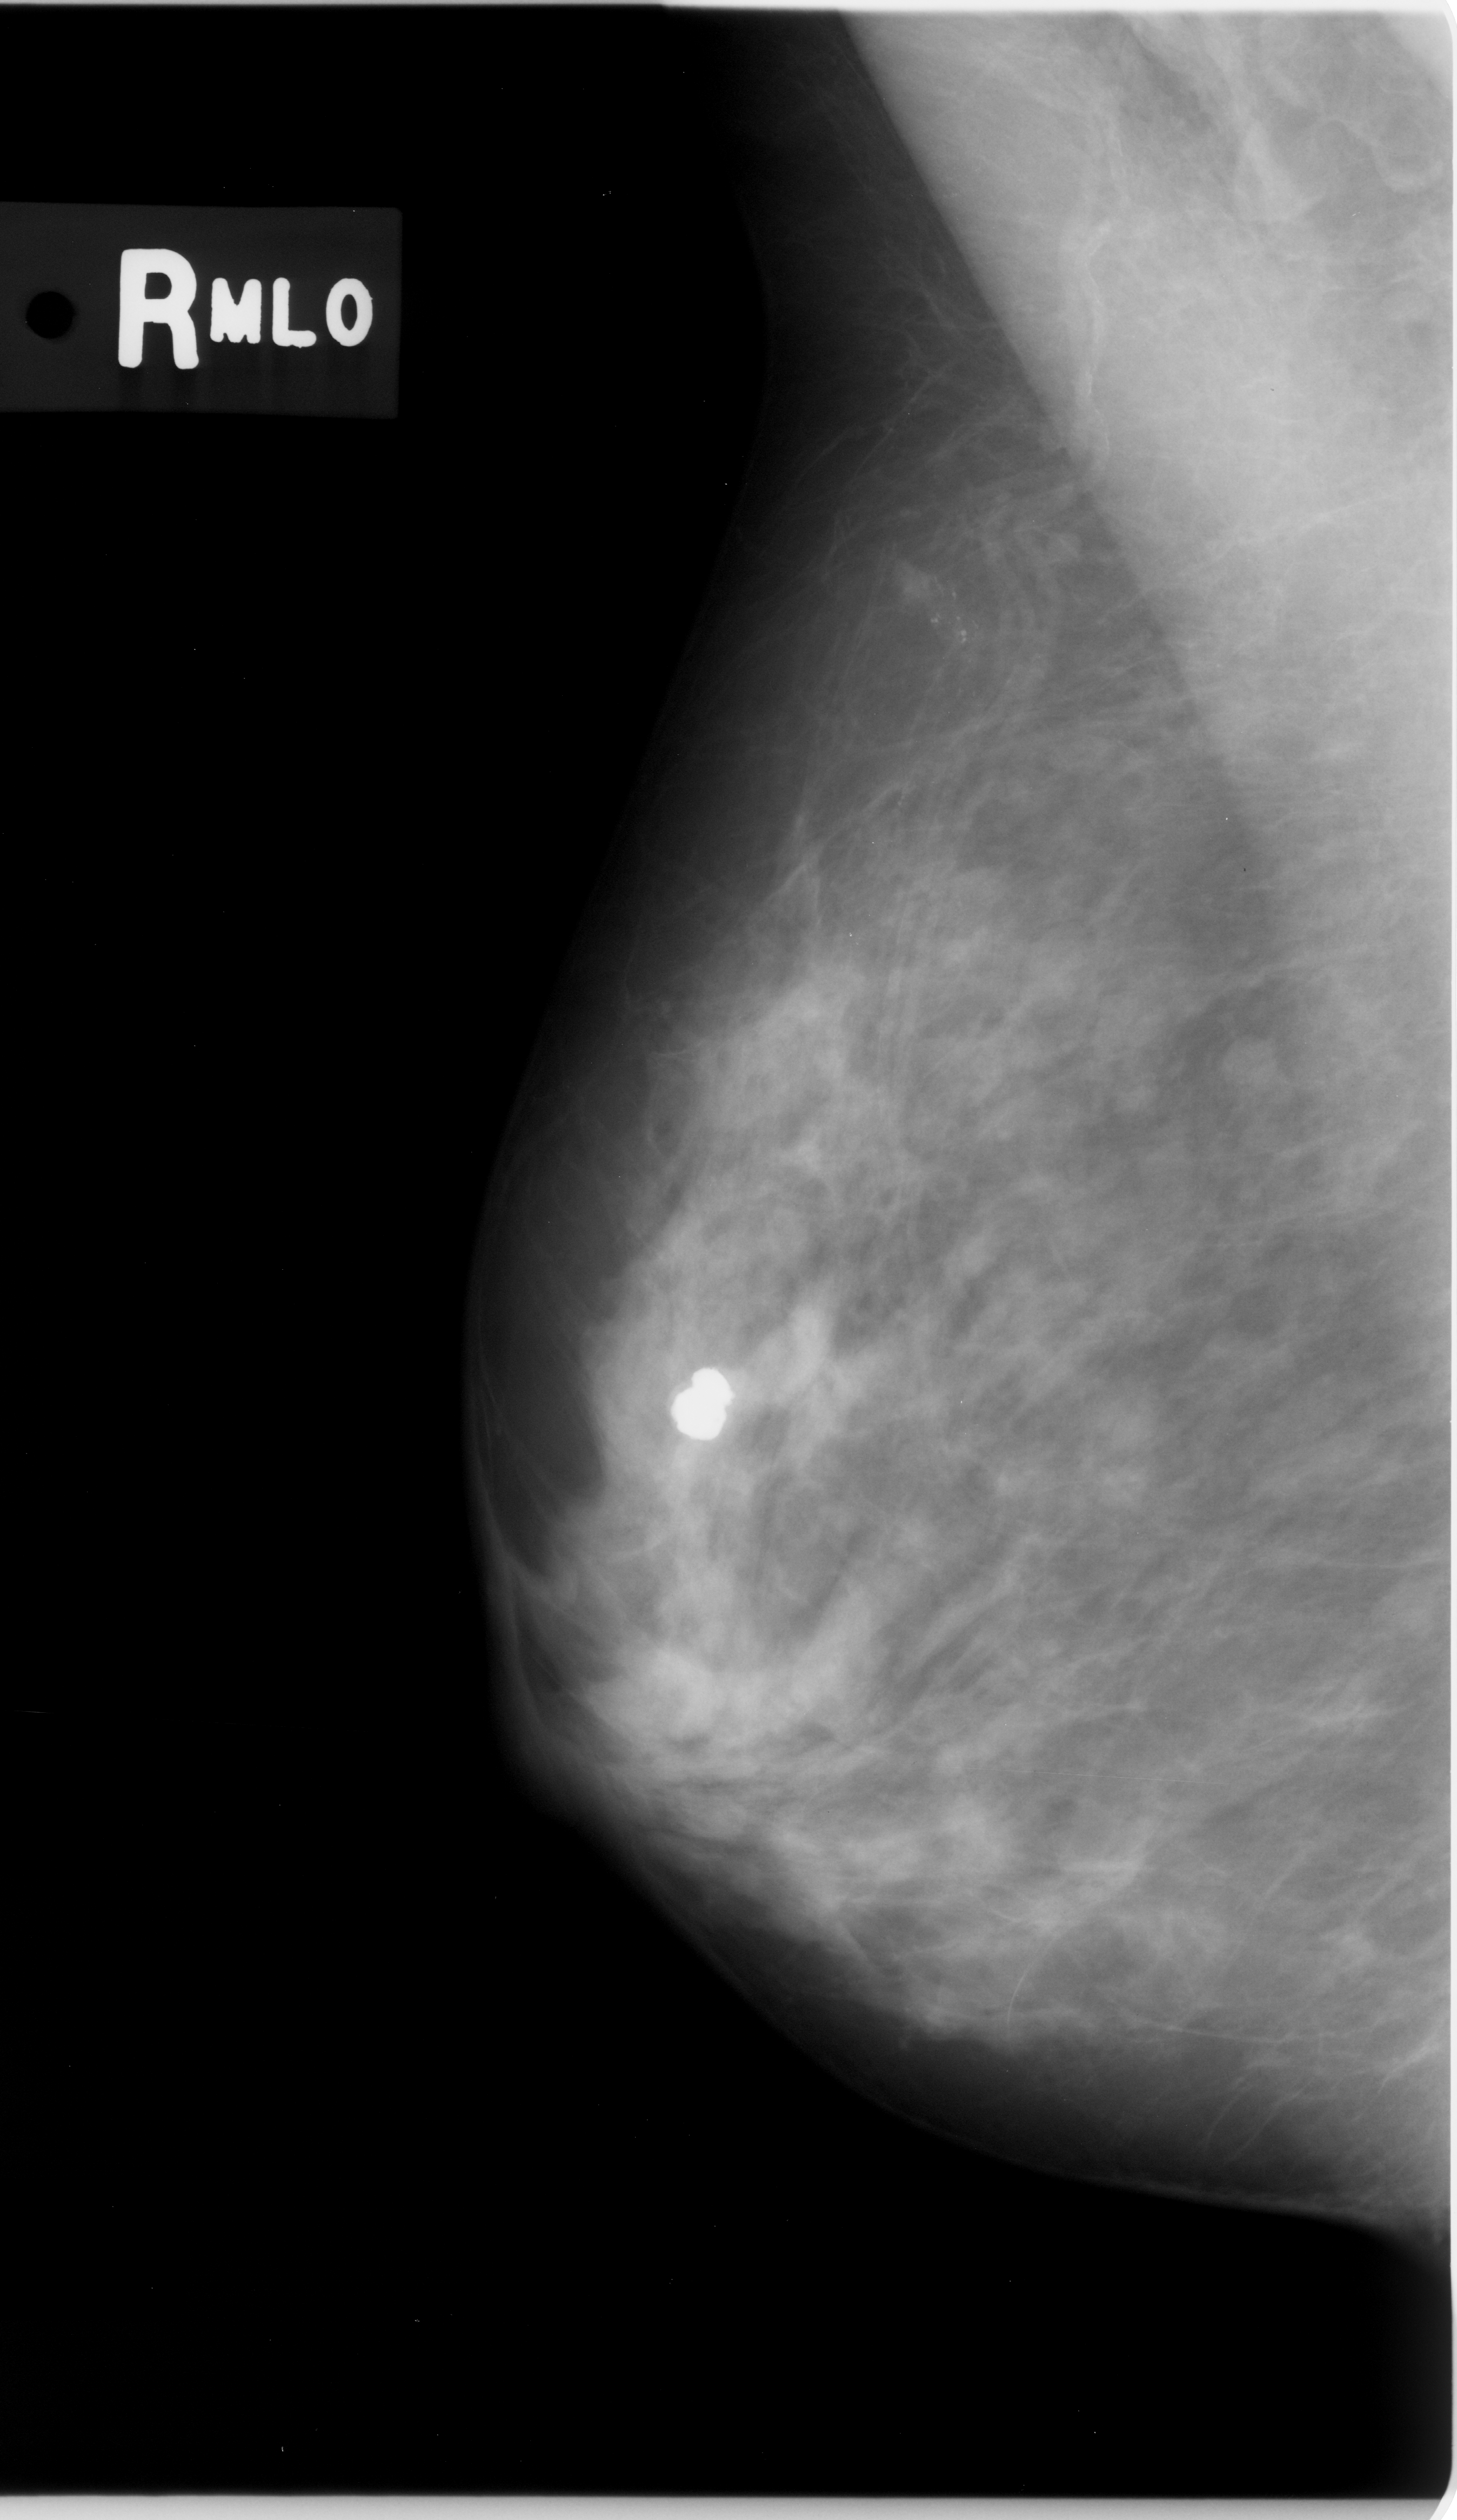
Digitized screen-film mammogram; right breast; MLO view; breast composition: heterogeneously dense (BI-RADS density category 3 of 4); 1457 × 2520 image matrix.
Expert-marked regions of interest on this film, with their recorded descriptors:
- calcifications, morphology pleomorphic, distribution clustered; BI-RADS assessment category 5; subtlety rating 4 on a 1 (subtle) to 5 (obvious) scale; pathology (as recorded): malignant: bounding box <864,531,1034,693> (left, top, right, bottom; pixels)